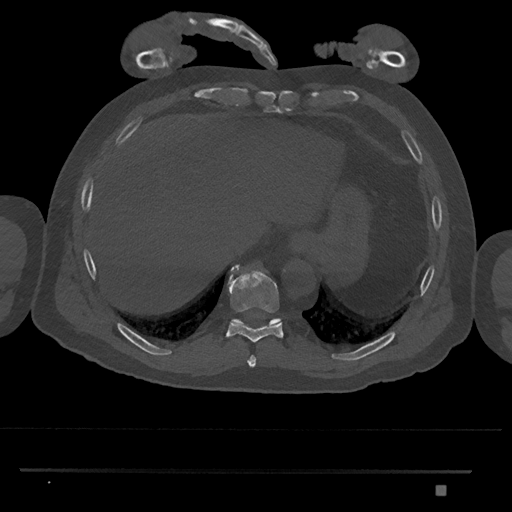
CT including the spine, one axial slice. Slice 1047 of 1134 in the series (ordered by position). Reconstruction kernel Br40s/3. Bone window (W 1800 / L 400 HU). 0.5 mm slice thickness. 512 × 512 image matrix, field of view 429 × 429 mm. Patient: male, 65 years. Case-level facts recorded for this patient, not image findings: primary cancer: prostate.
Structures marked on this image (semi-automatic segmentation, software-assisted and operator-edited):
- T10 vertebra: bounding box <232,318,281,324> (left, top, right, bottom; pixels)
- T8 vertebra: <247,355,256,367>
- T9 vertebra: <226,264,284,343>